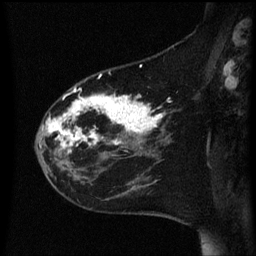
Breast MRI (dynamic contrast-enhanced), one sagittal slice; position 19 of 60 along the scan axis; dynamic contrast-enhanced series, image 2 of 3 at this slice position (ordered by acquisition); 1.5 T; TE 4.2 ms, TR 8.4 ms; 2.2 mm slice thickness; 256 × 256 image matrix. Female patient, age 35 years. Case-level facts recorded for this patient, not image findings: setting: breast cancer imaged before/during neoadjuvant chemotherapy; receptor status: HER2-positive.
Annotated regions visible in this slice (semi-automatically segmented with operator editing):
- analysis volume of interest (the breast-tissue region the enhancement analysis was run in; not a lesion): box from (x=36, y=78) to (x=173, y=163) px
- tumour enhancement mask (voxels above the 70 % enhancement threshold inside the analysis volume of interest): (x=44, y=88)–(x=165, y=153)